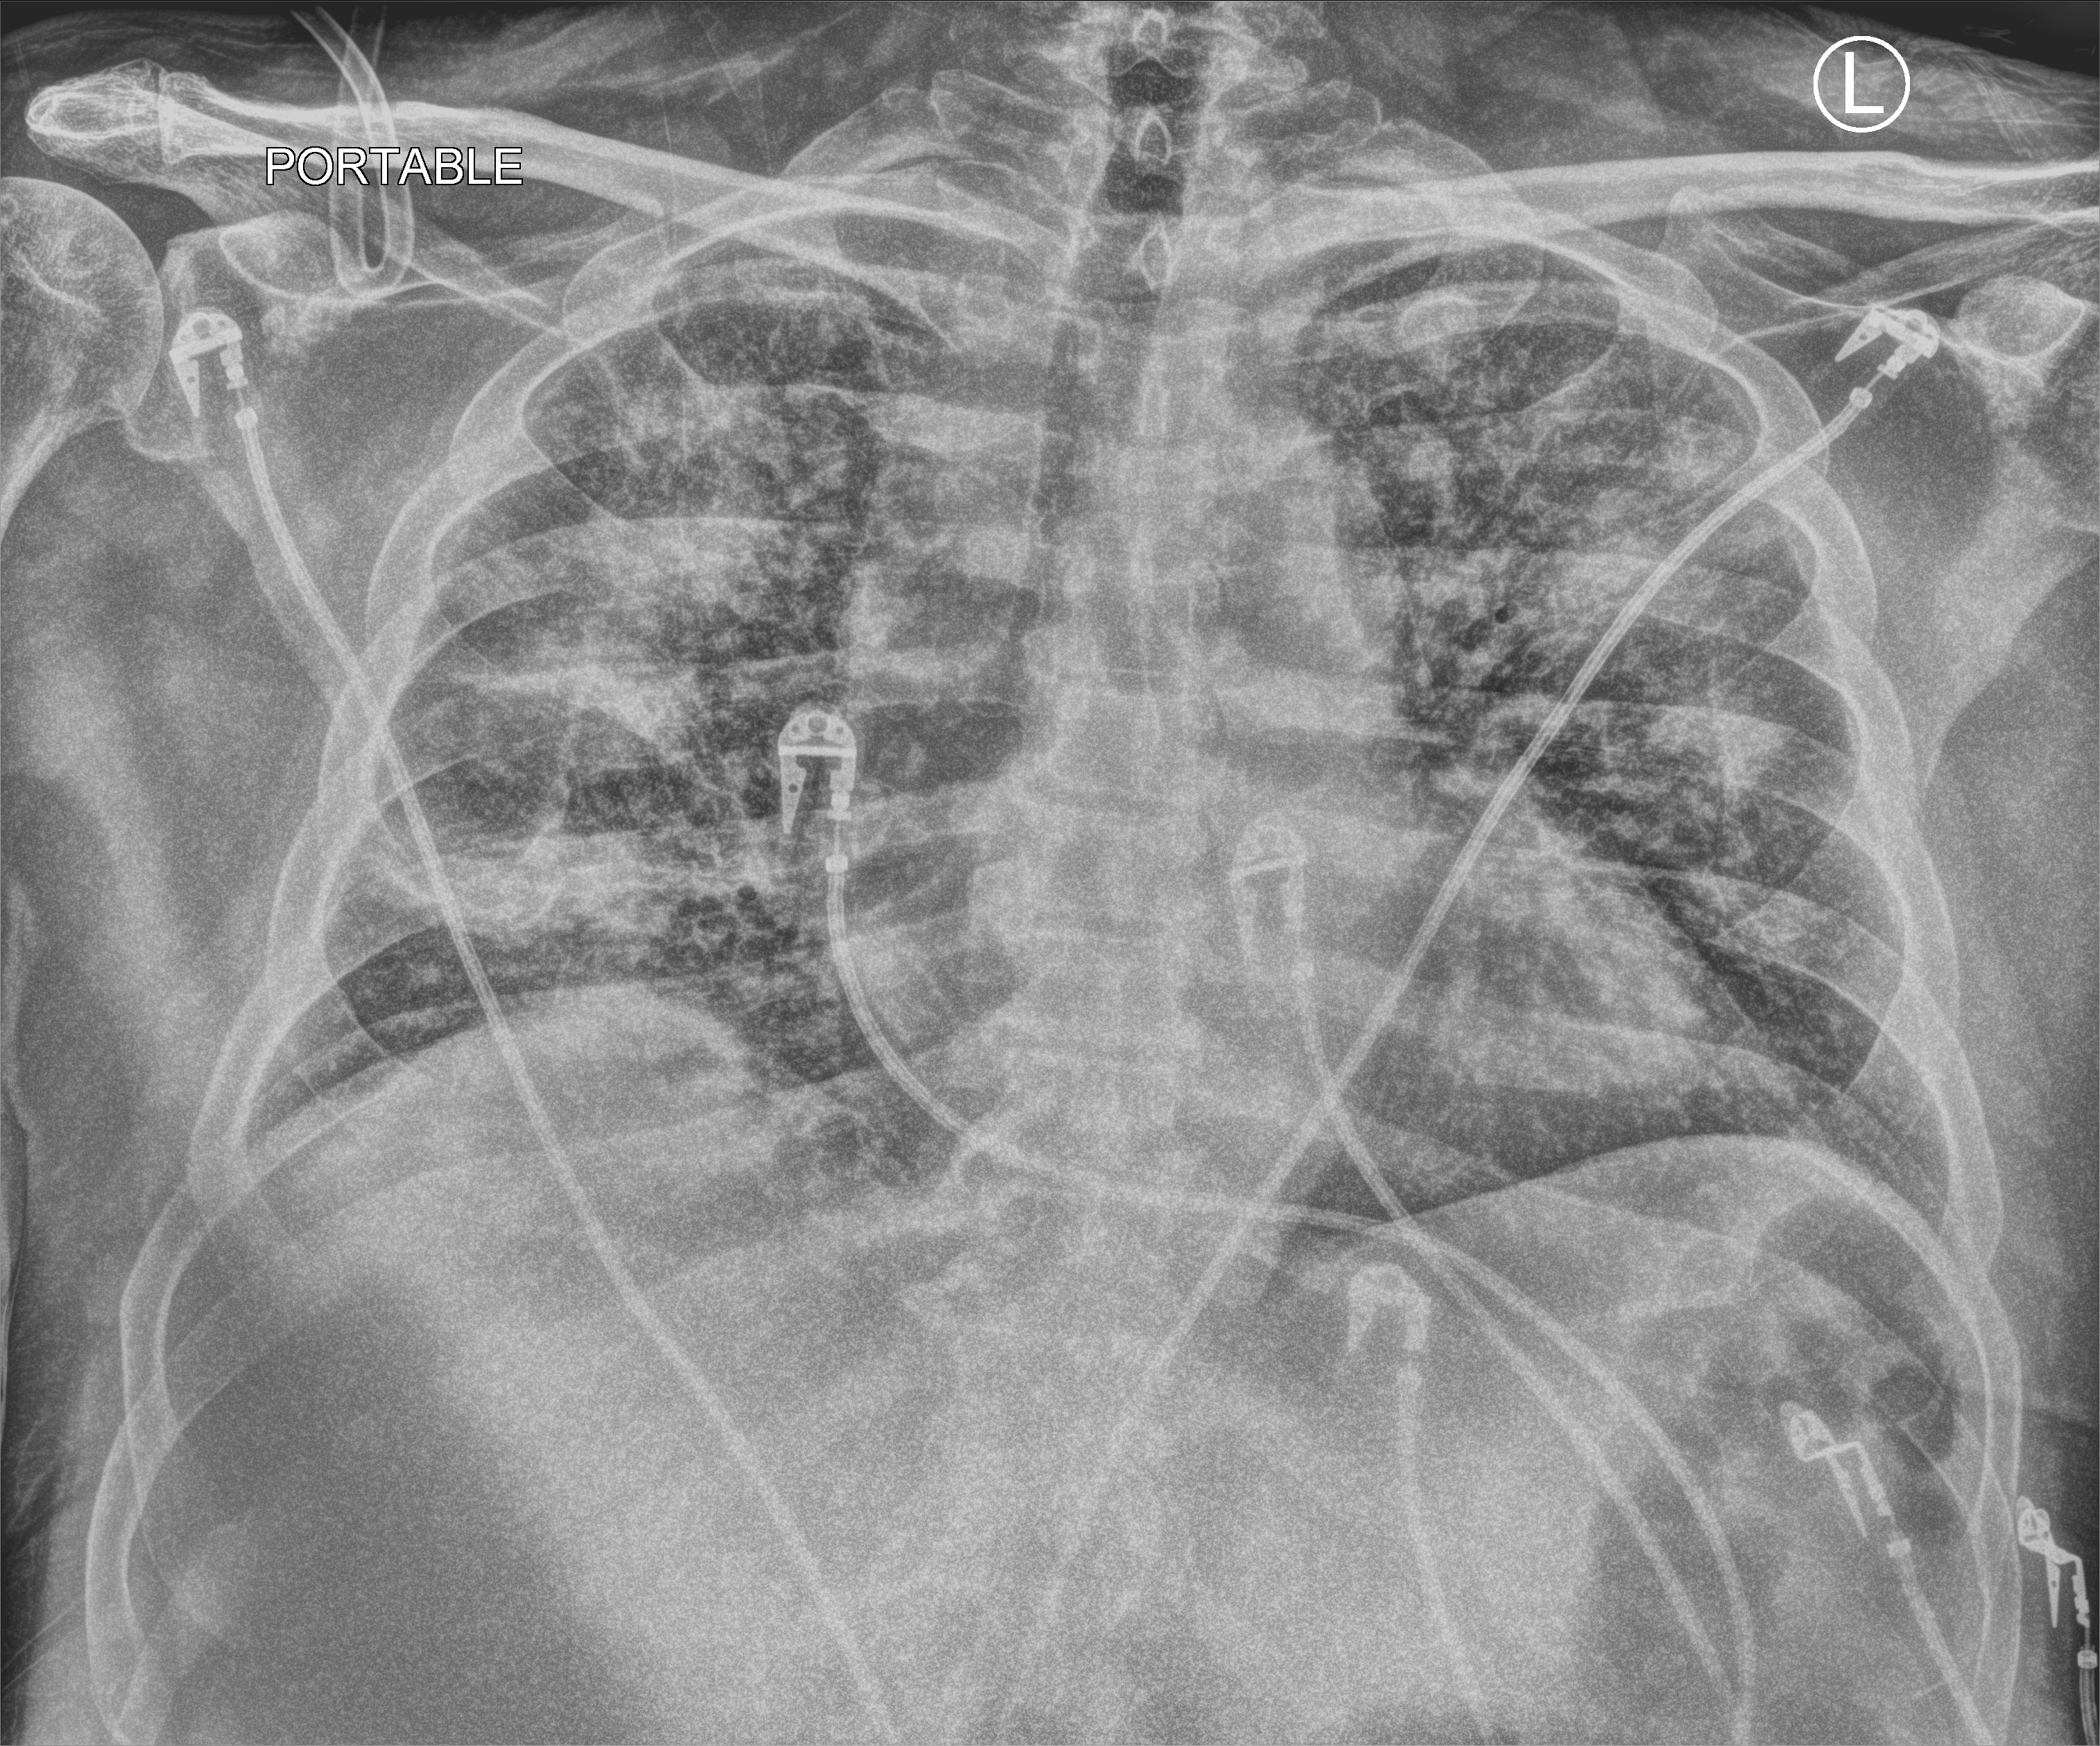
Portable chest radiograph; anteroposterior (AP) projection. Patient hospitalised with COVID-19; male, aged 60–74 years.
Hospital-stay facts (about this admission, not read from this image; timing relative to this image not recorded): length of hospital stay: 33 days.